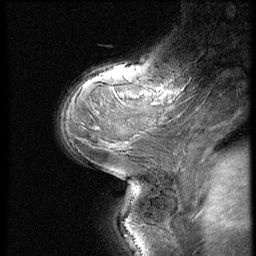
Breast MRI (dynamic contrast-enhanced), one sagittal slice; slice 39 of 56 in the series (ordered by position); 3 images stored at this slice position (order not interpretable as contrast timing); 1.5 T; TE 4.2 ms, TR 9 ms; 256 × 256 image matrix, field of view 180 × 180 mm. Patient: female, 54 years. From the clinical record (not read from this slice): setting: breast cancer imaged before/during neoadjuvant chemotherapy; receptor status: triple-negative.
Outlined on this slice (semi-automatic segmentation, software-assisted and operator-edited):
- analysis volume of interest (the breast-tissue region the enhancement analysis was run in; not a lesion): box from (x=141, y=76) to (x=199, y=121) px
- tumour enhancement mask (voxels above the 140 % enhancement threshold inside the analysis volume of interest): (x=174, y=91)–(x=178, y=95)